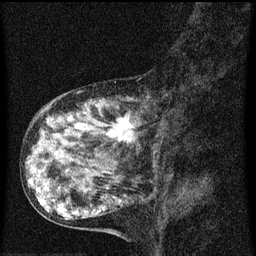
Breast MRI (dynamic contrast-enhanced), one sagittal slice; dynamic contrast-enhanced series, image 2 of 3 at this slice position (ordered by acquisition); 1.5 T; TE 4.2 ms, TR 8 ms; 2 mm slice thickness; 256 × 256 image matrix, field of view 180 × 180 mm. Female patient, age 55 years.
Outlined on this slice (semi-automatically segmented with operator editing):
- analysis volume of interest (the breast-tissue region the enhancement analysis was run in; not a lesion): bounding box [x1, y1, x2, y2] px = [38, 92, 171, 159]
- tumour enhancement mask (voxels above the 70 % enhancement threshold inside the analysis volume of interest): [48, 116, 137, 143]